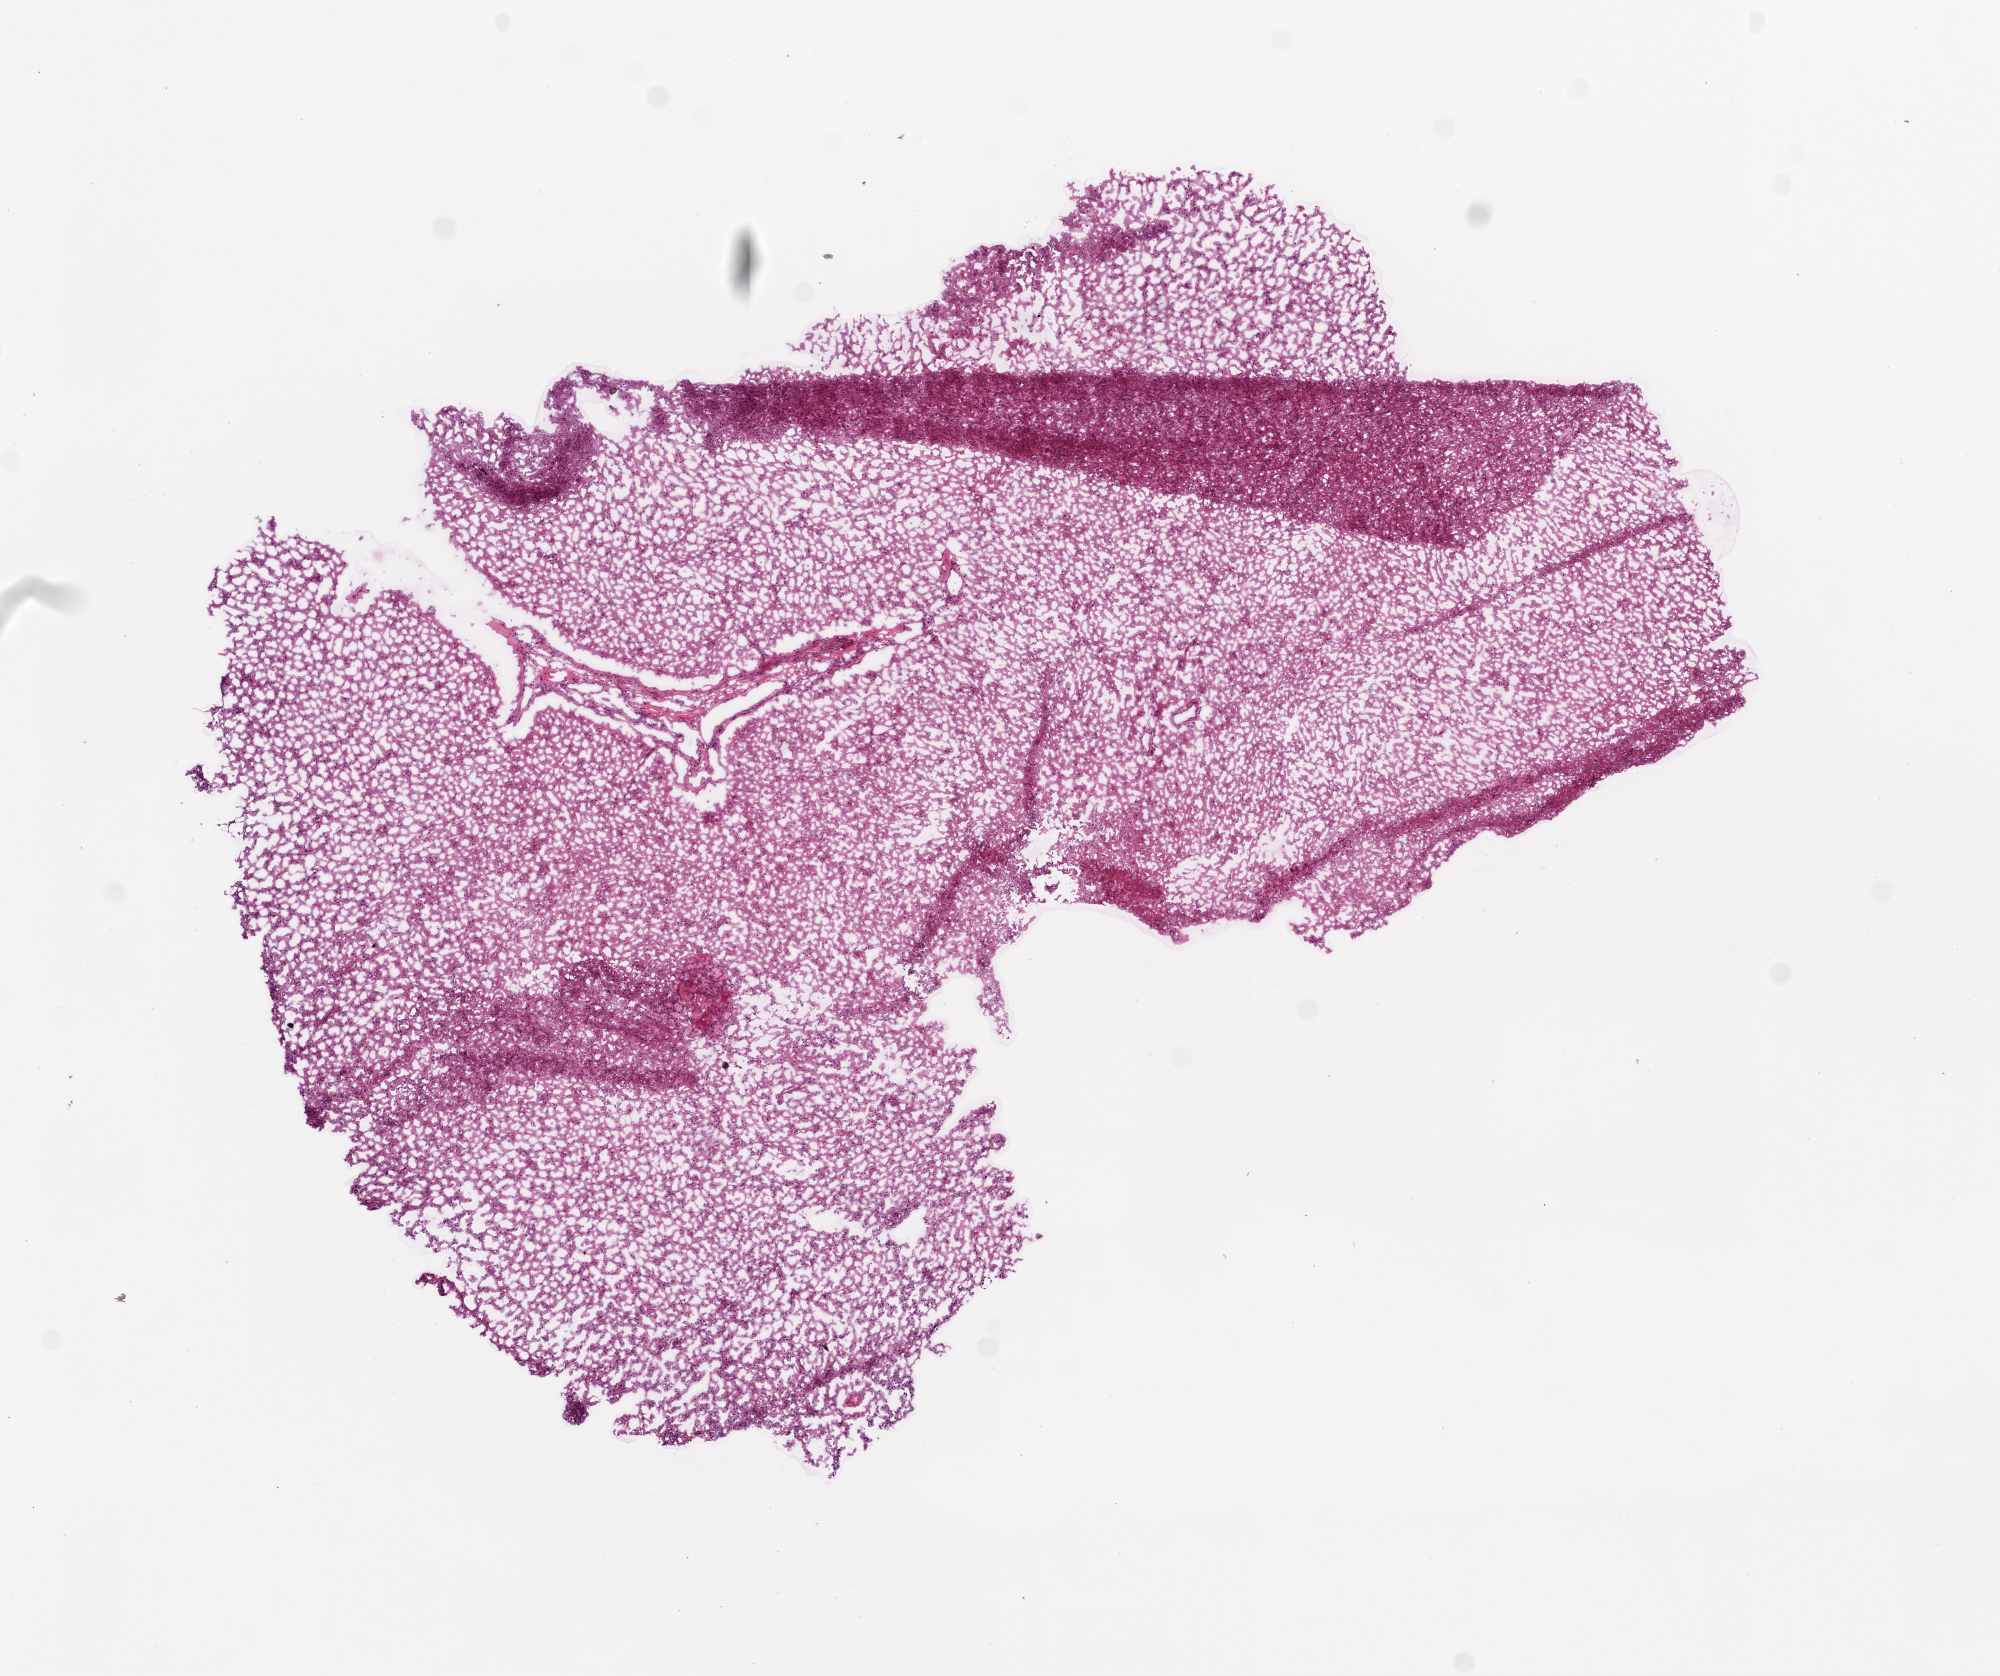
H&E whole-slide image, shown as a low-resolution overview of the whole scanned area (about 8.0 x 6.7 mm, from a 20x scan). Frozen section from the bottom of the tissue portion. Primary tumour sample from the brain. Patient: male, age at initial diagnosis 52 years. Slide review estimates, as recorded: tumour cells 100%, tumour nuclei 80%, normal cells 0%, stromal cells 0%, necrosis 0%.
Histologic diagnosis: Glioblastoma.